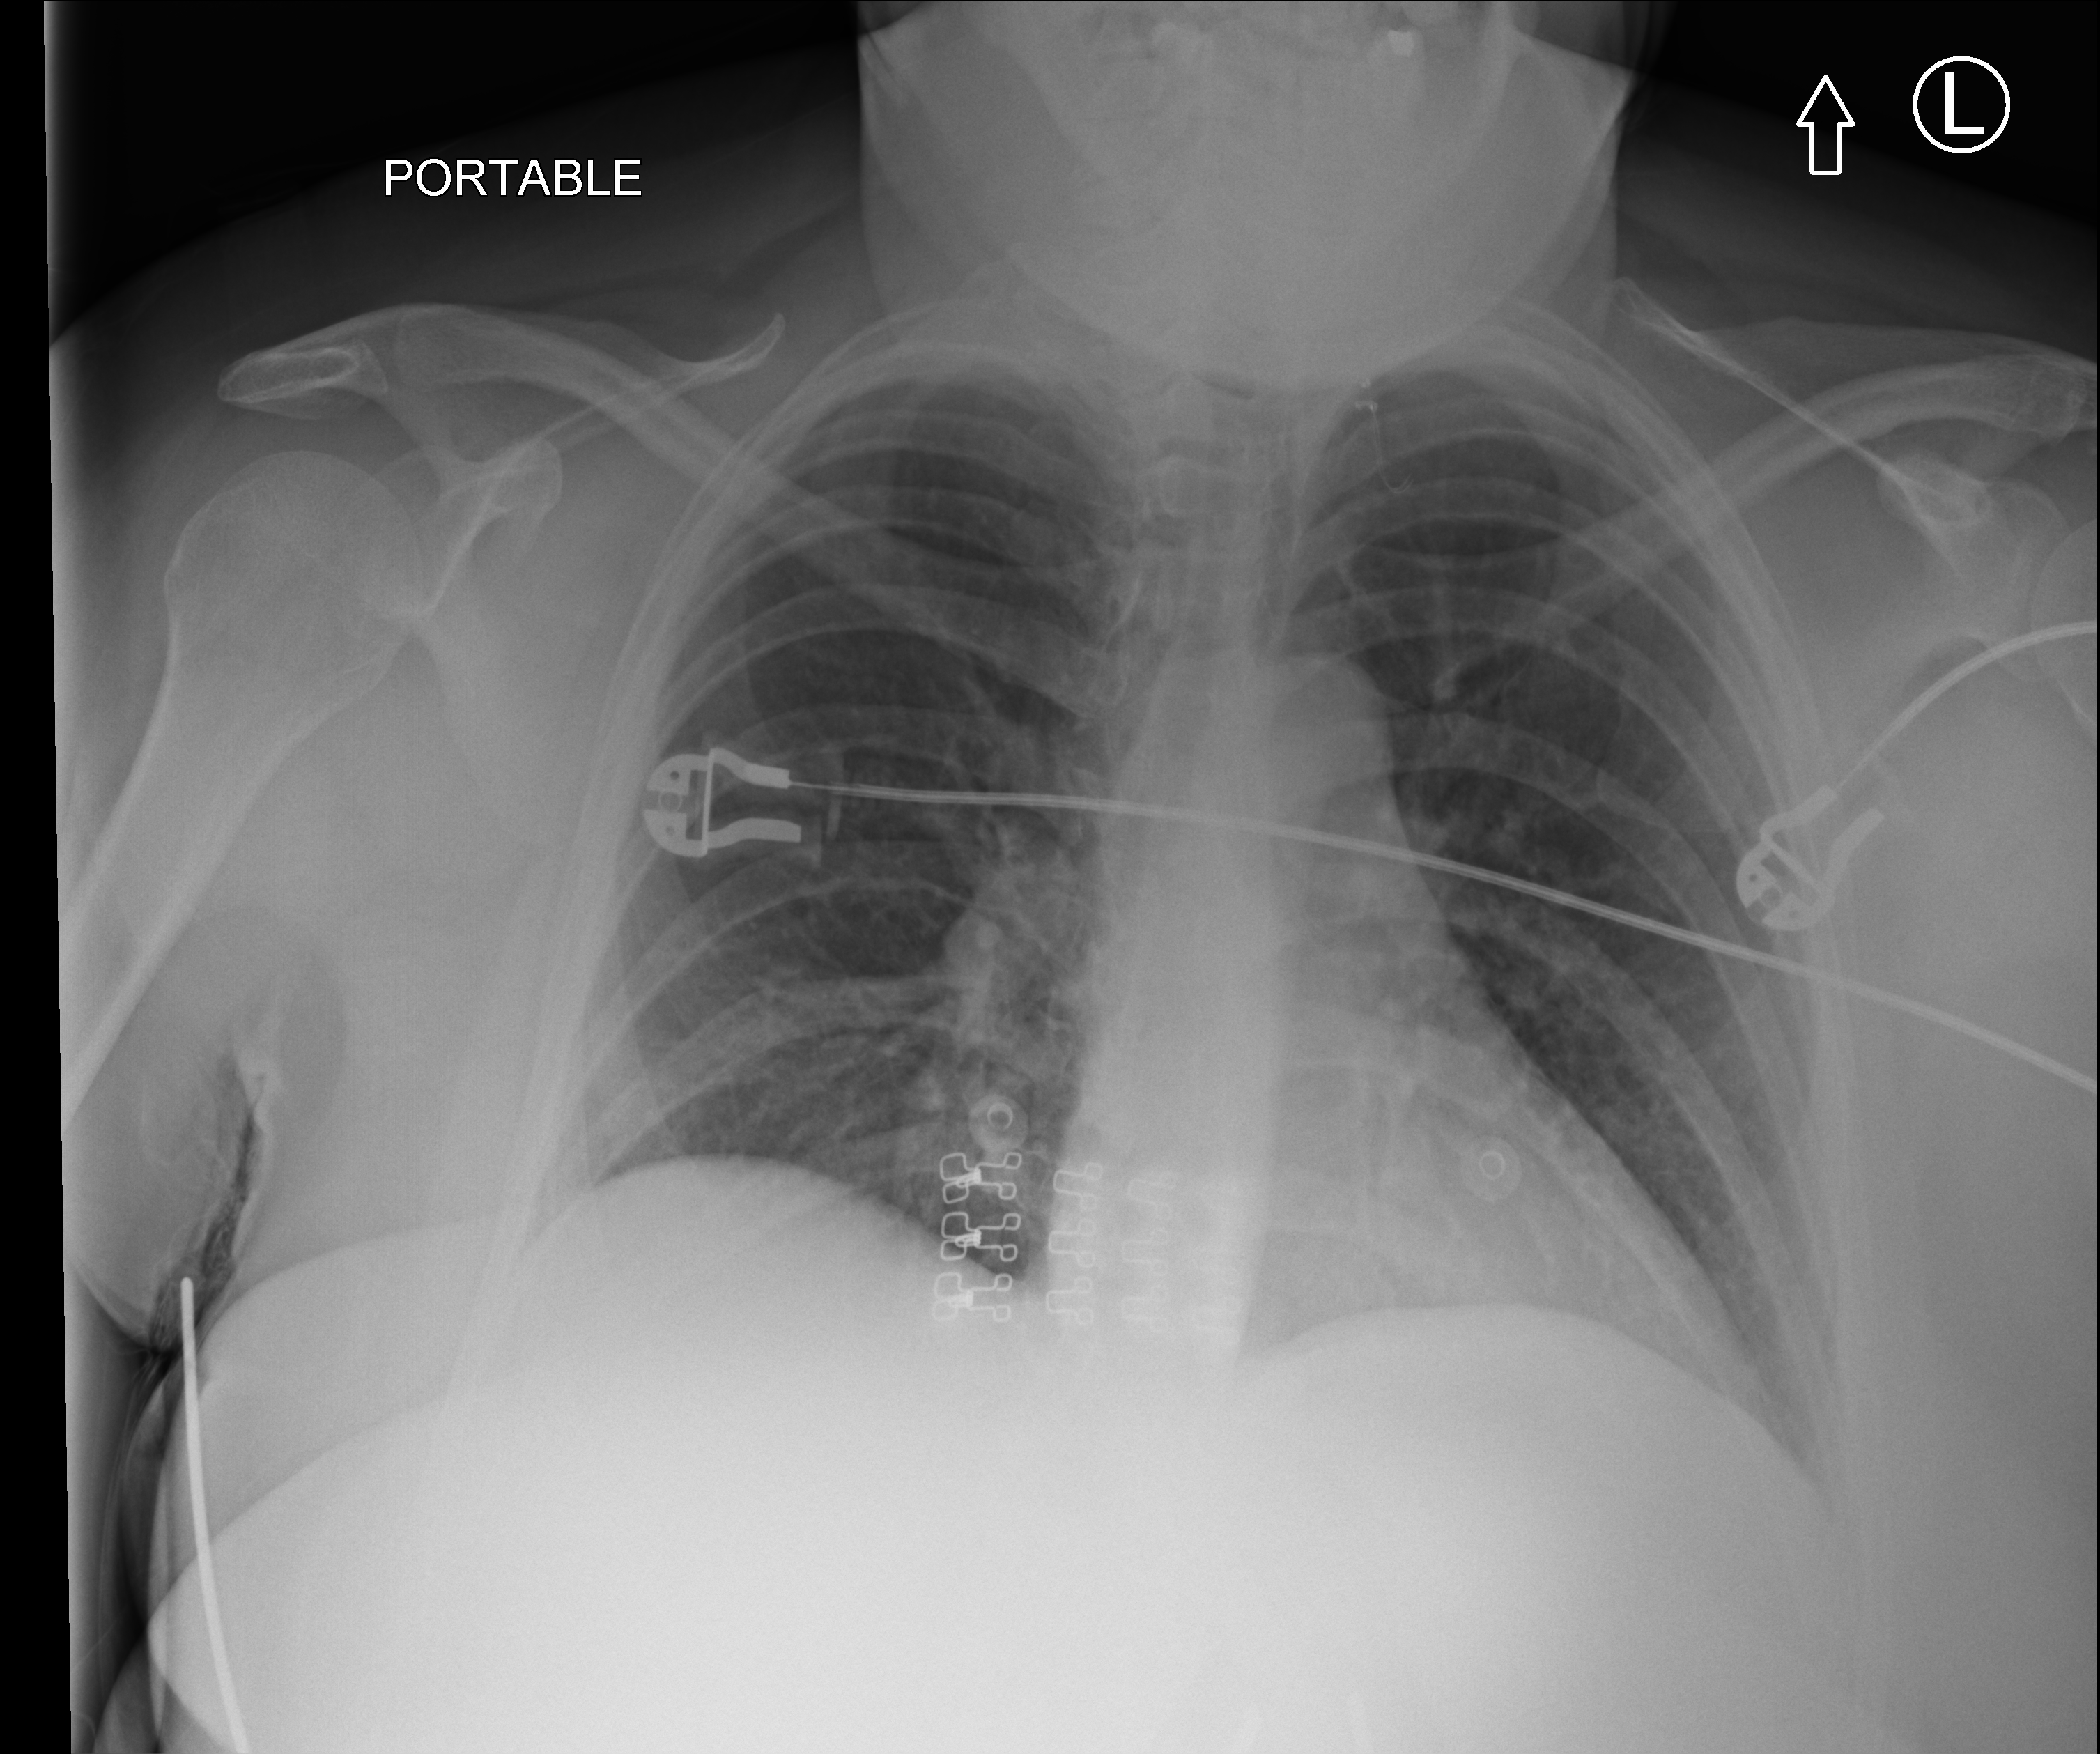
Chest X-ray (portable); anteroposterior (AP) projection. Patient hospitalised with COVID-19; female, aged 18–59 years.
Hospital-stay facts (about this admission, not read from this image; timing relative to this image not recorded):
- smoking status (admission record): never
- diabetes (admission record): no